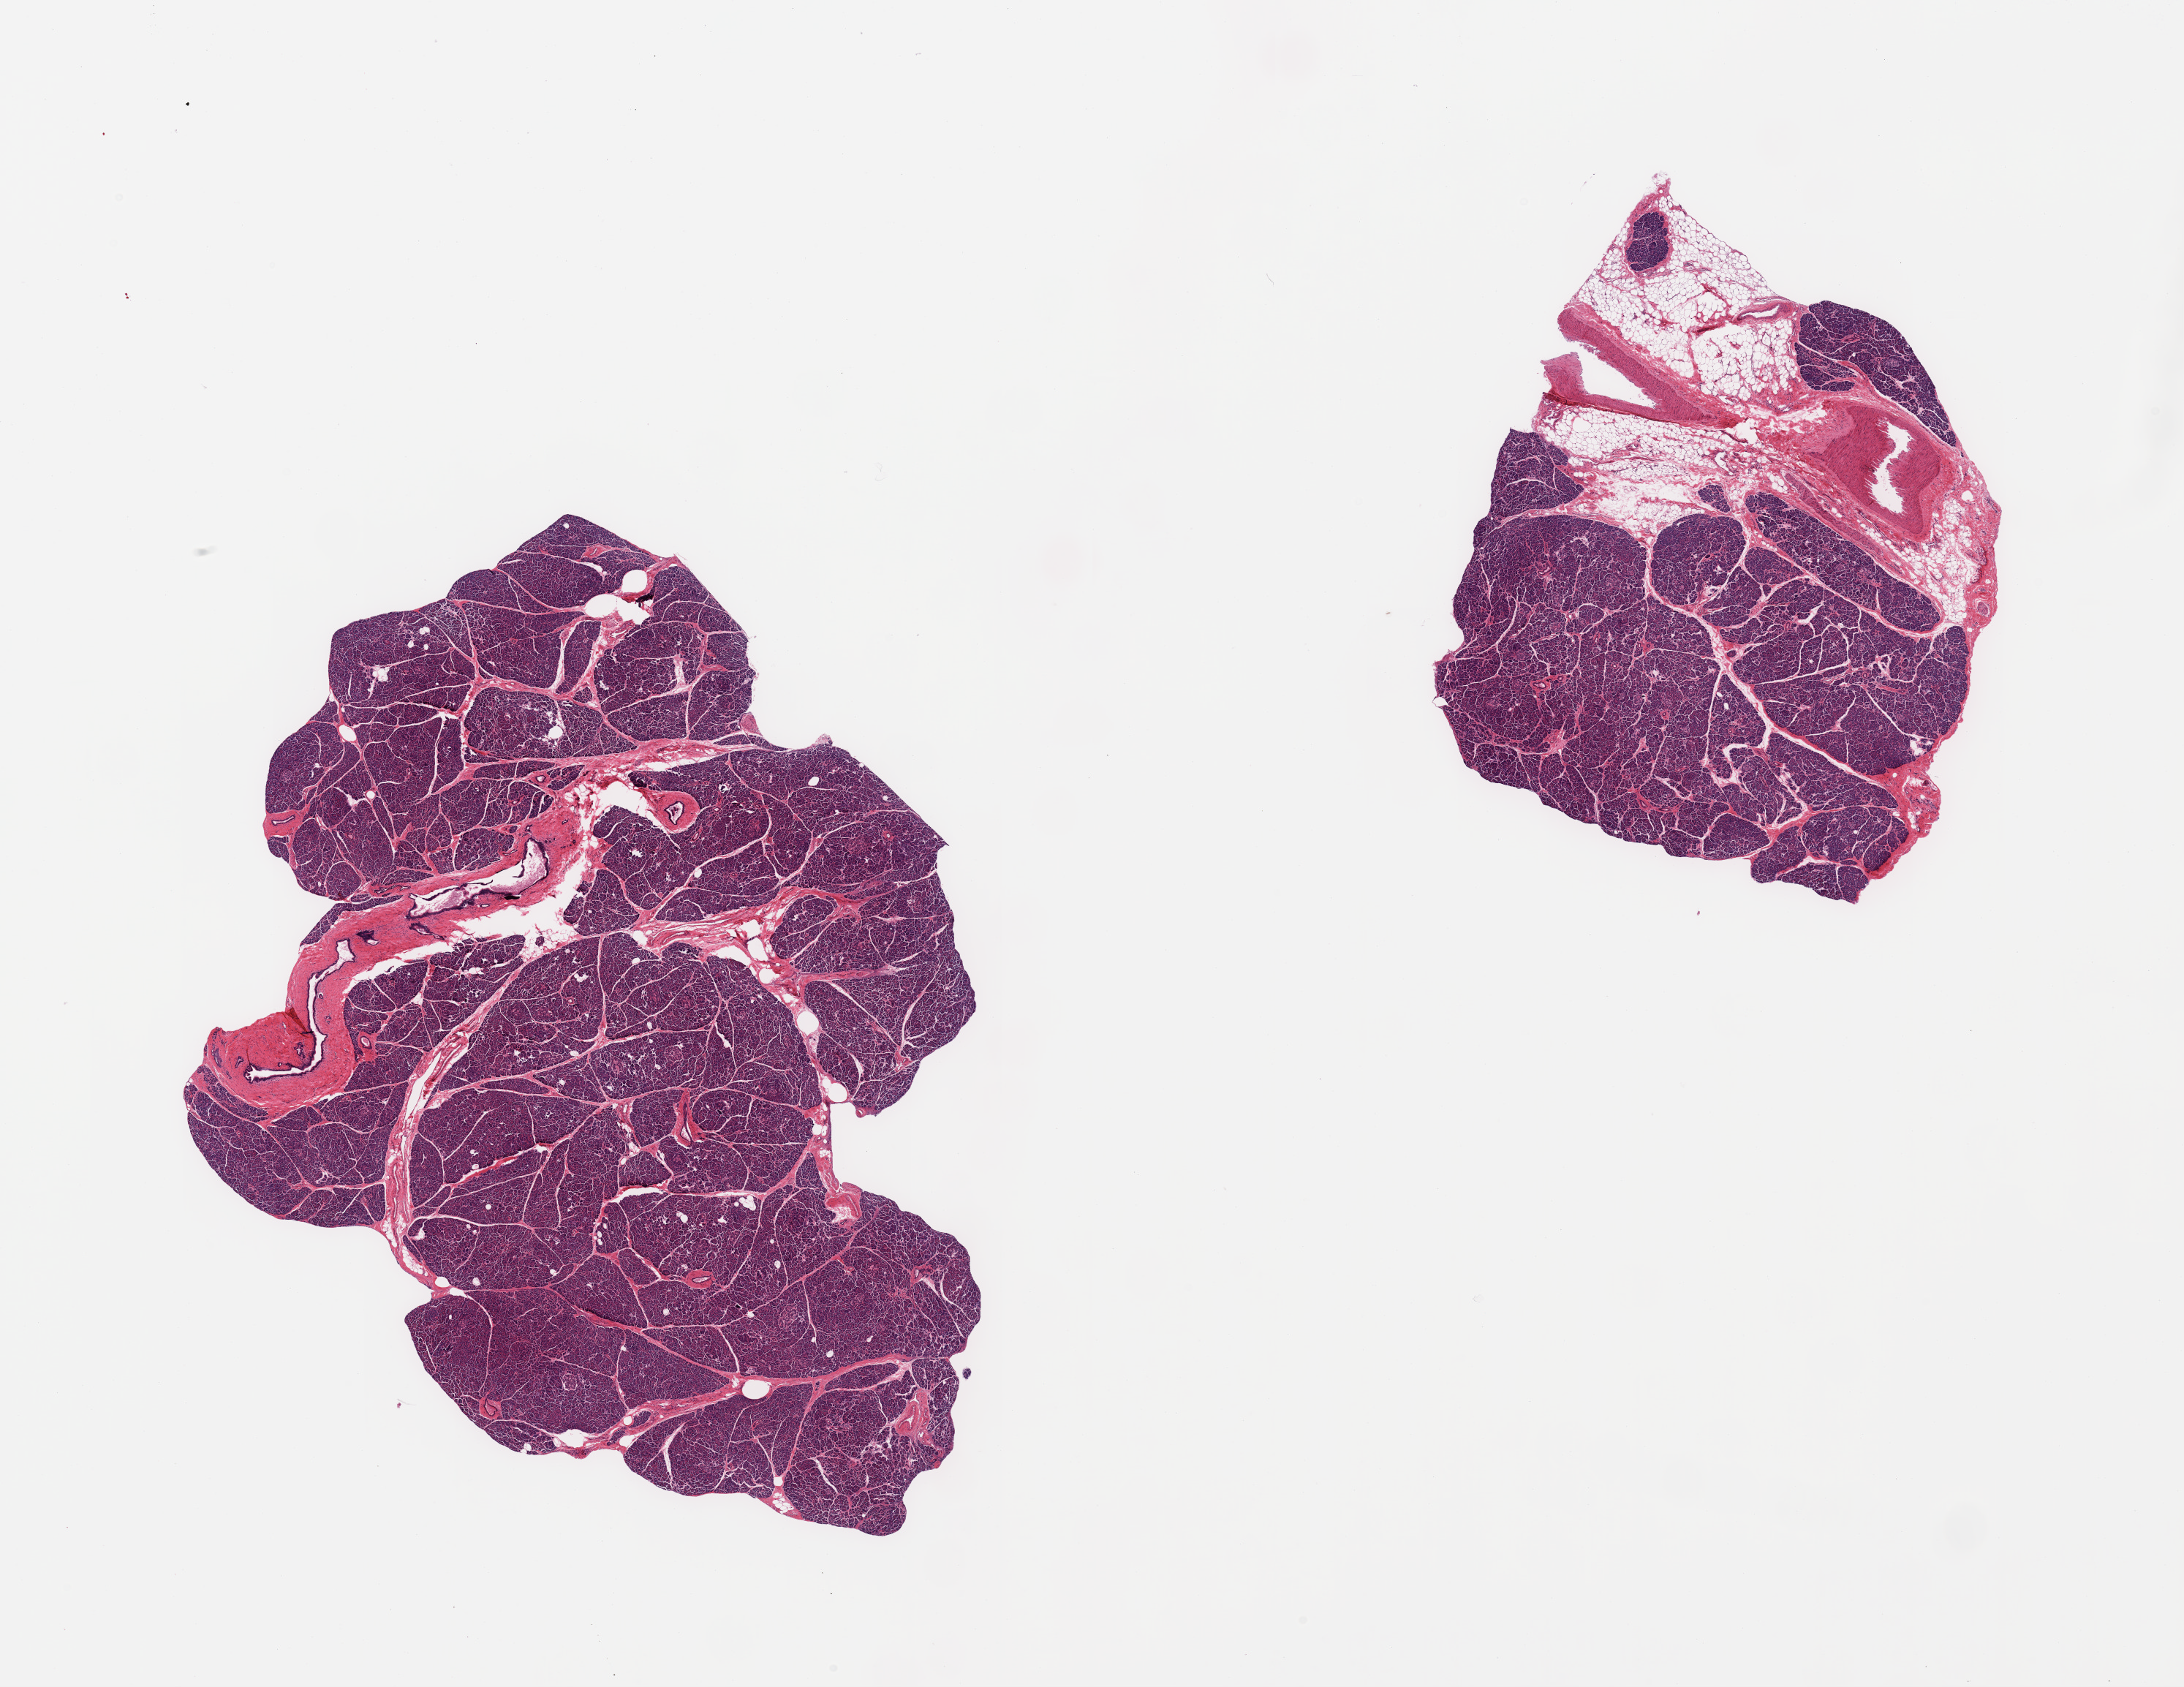
Whole-slide image, haematoxylin and eosin stain, brightfield — whole scanned area (about 23.6 x 18.2 mm) shown as a low-resolution overview. PAXgene-fixed paraffin-embedded (PFPE) section. Sampled site (target tissue): pancreas. Donor tissue sample. Donor: male.
- pathologist's review note for this sample: 2 pieces; Islets relatively well preserved, low-moderate numbers